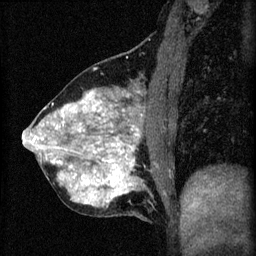
Breast MRI (dynamic contrast-enhanced), one sagittal slice; slice 24 of 60 in the series (ordered by position); 3 images stored at this slice position (order not interpretable as contrast timing); 1.5 T; TE 4.2 ms, TR 8.2 ms; 2 mm slice thickness; 256 × 256 image matrix. Patient: female, 40 years.
Outlined on this slice (semi-automatically segmented with operator editing):
- analysis volume of interest (the breast-tissue region the enhancement analysis was run in; not a lesion): bounding box [x1, y1, x2, y2] px = [24, 76, 171, 219]
- tumour enhancement mask (voxels above the 70 % enhancement threshold inside the analysis volume of interest): [24, 92, 143, 205]